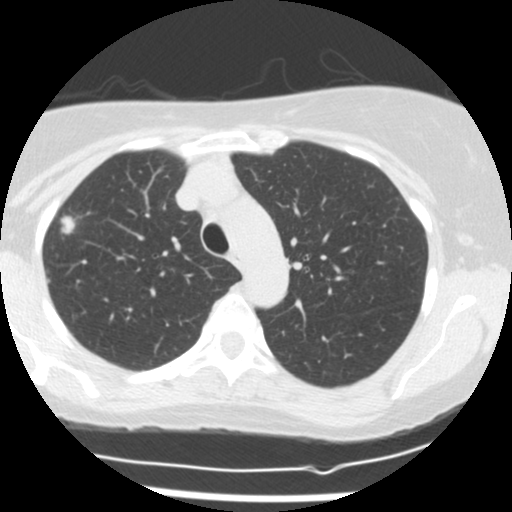
Low-dose screening chest CT, one axial slice. Slice 117 of 160 in the series (ordered by position). Lung window (W 1500 / L -600 HU). 2.5 mm slice thickness. 512 × 512 image matrix, field of view 300 × 300 mm.
Structures marked on this image (outlined manually by an expert reader):
- lesion 1 (tumor, upper lobe of right lung): box from (x=61, y=216) to (x=76, y=234) px